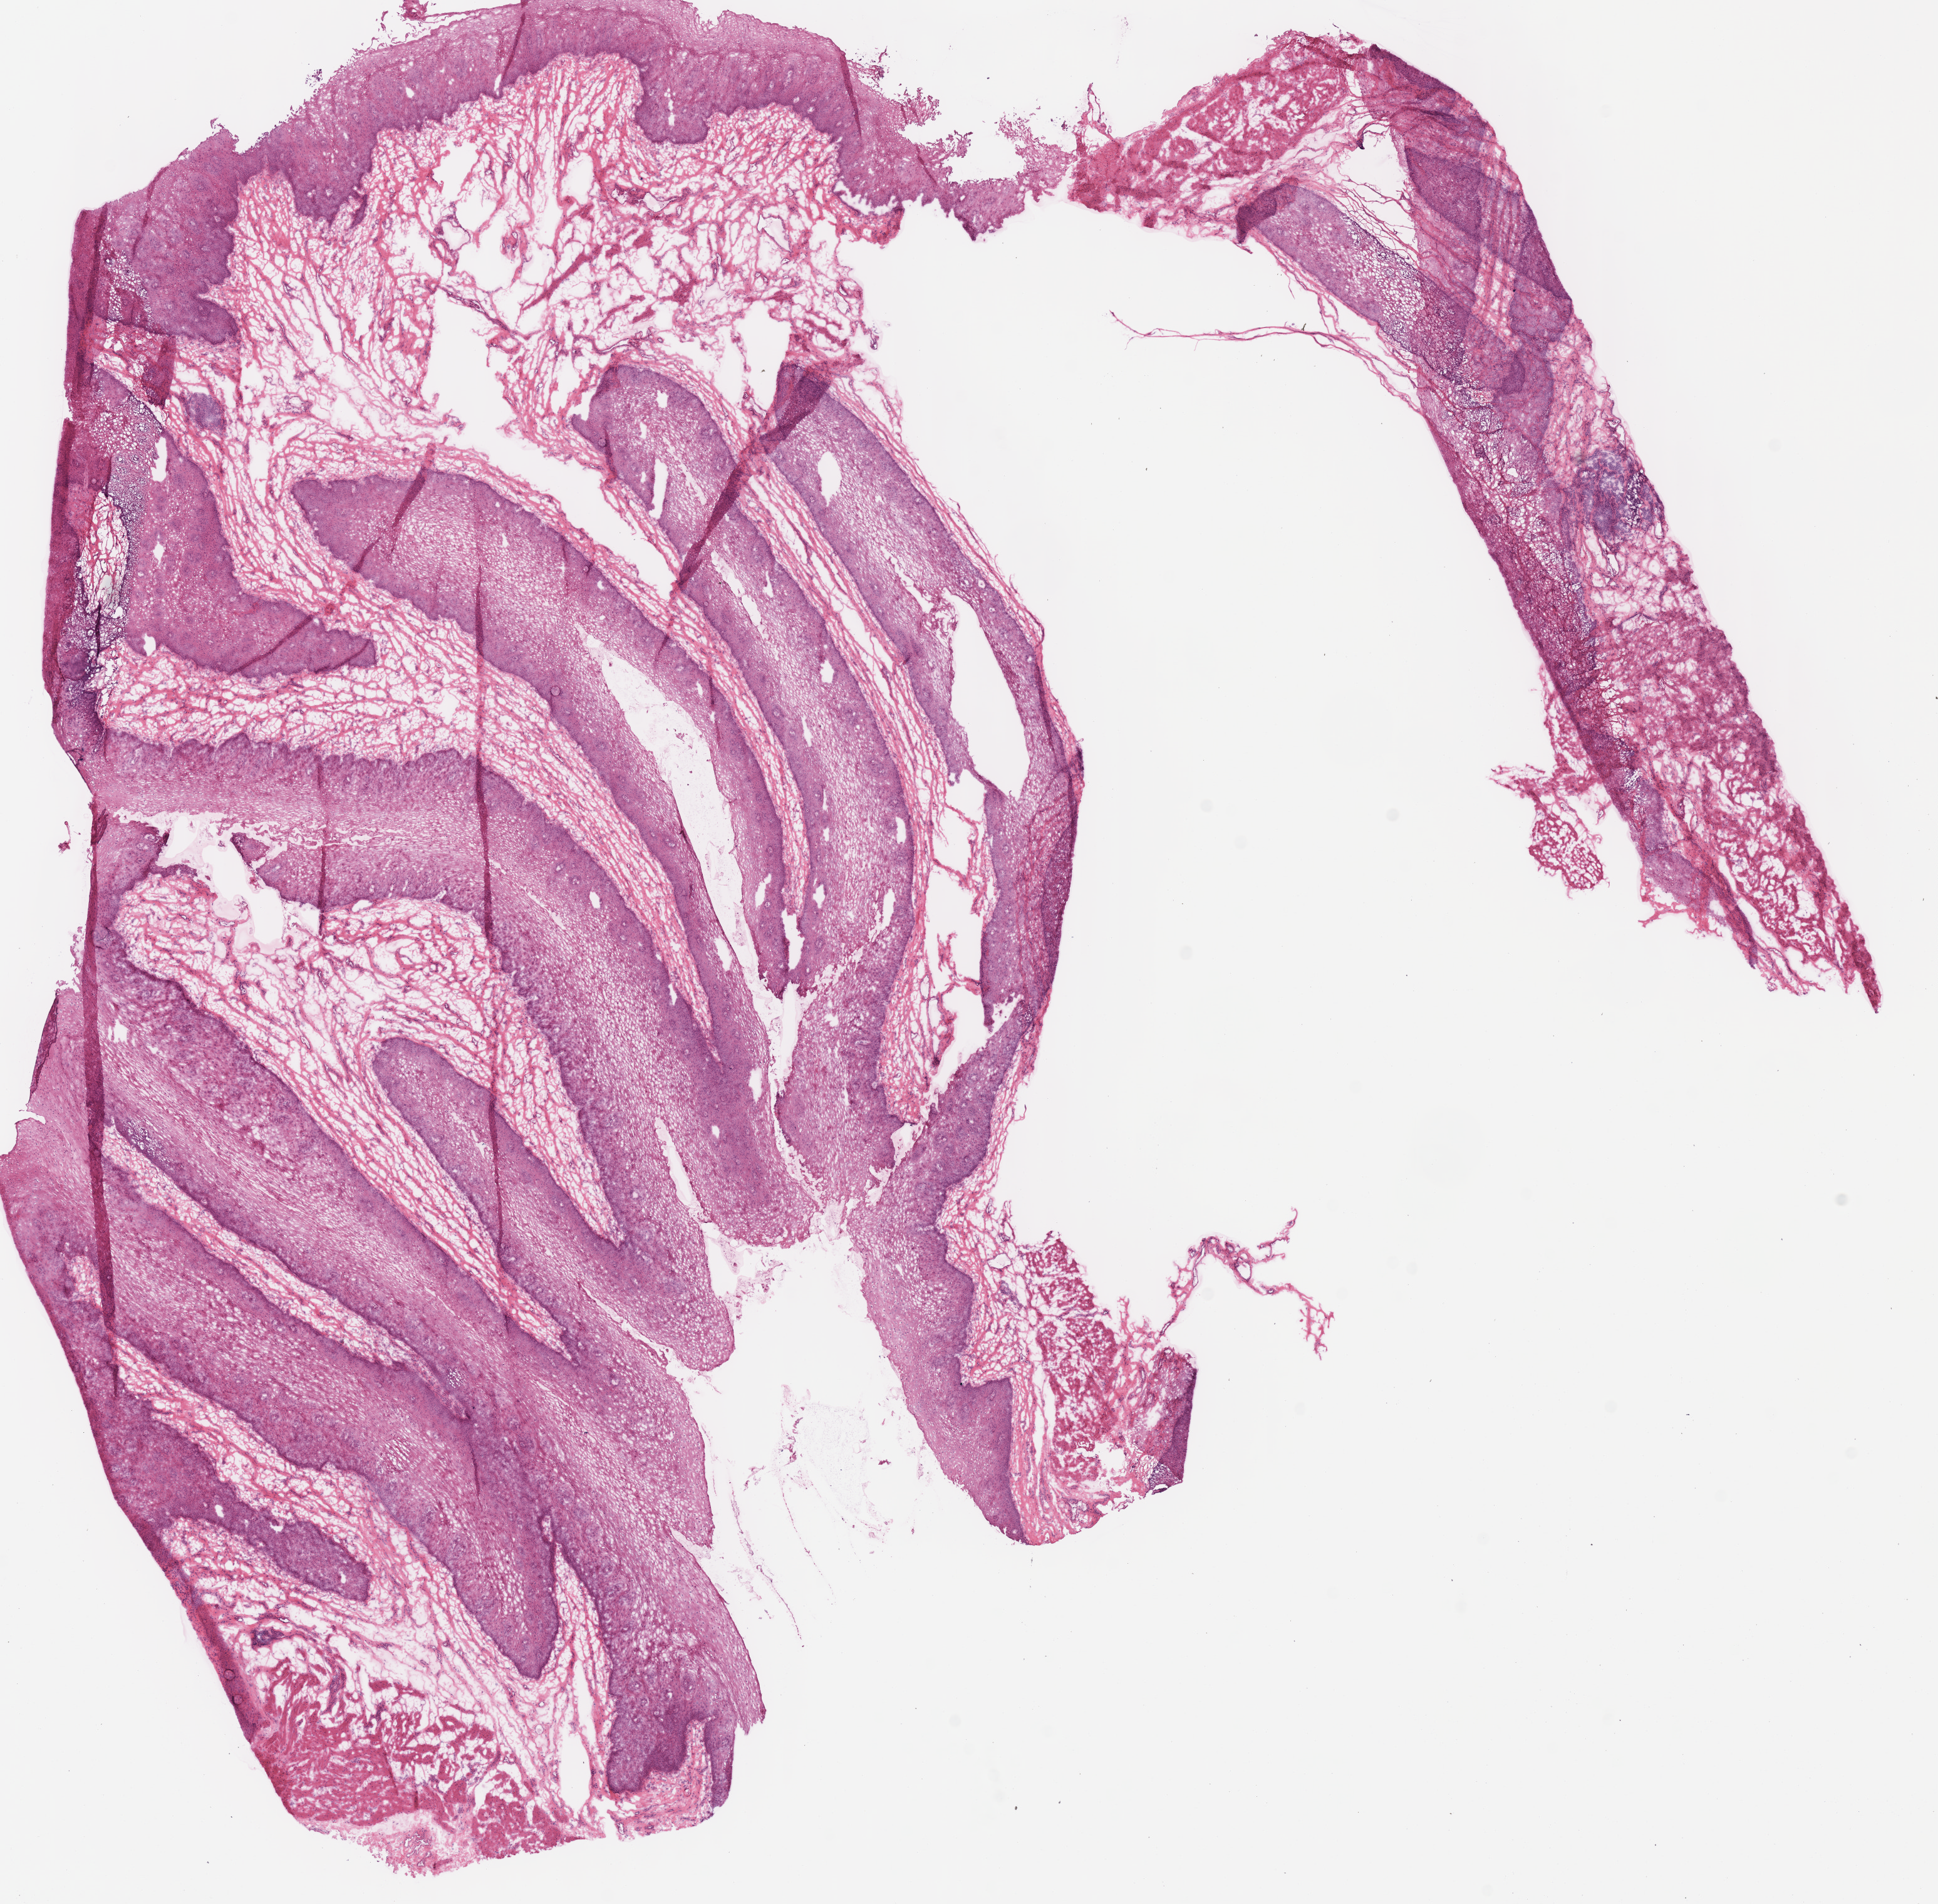
Hematoxylin and eosin (H&E) stained whole-slide image, shown as a low-resolution overview of the whole scanned area (about 12.2 x 12.0 mm, from a 40x scan). Frozen section from the top of the tissue portion. Sample: solid tissue normal (non-tumour tissue), stomach. Male, age 50 years at initial diagnosis. Infiltration values recorded for this section: lymphocyte infiltration 2%, monocyte infiltration 0%, neutrophil infiltration 0%.
This section: solid tissue normal sample (biorepository sample class). Patient diagnosis: Carcinoma, diffuse type (cardia, NOS).